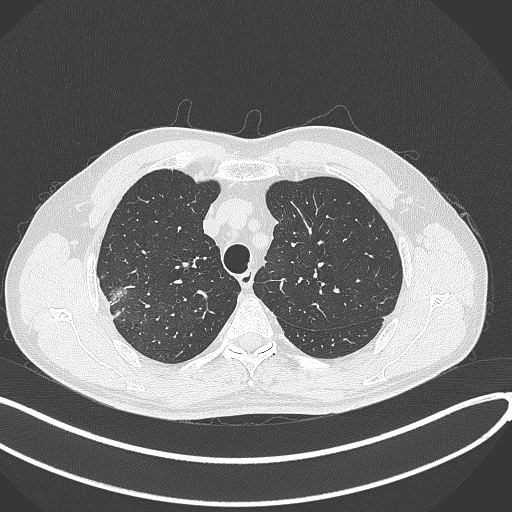
Chest CT, one axial slice; position 333 of 381 along the scan axis; reconstruction kernel B70f; 120 kVp; lung window (W 1500 / L -600 HU); 512 × 512 image matrix, field of view 400 × 400 mm. Patient: male, 62 years. Case-level facts recorded for this patient, not image findings: clinical TNM (as recorded): T1c N0 M0; histopathological grade: G2-3.
Structures marked on this image (bounding box drawn by a radiologist):
- lung tumour (recorded histology: adenocarcinoma): bounding box [x1, y1, x2, y2] px = [108, 281, 130, 318]